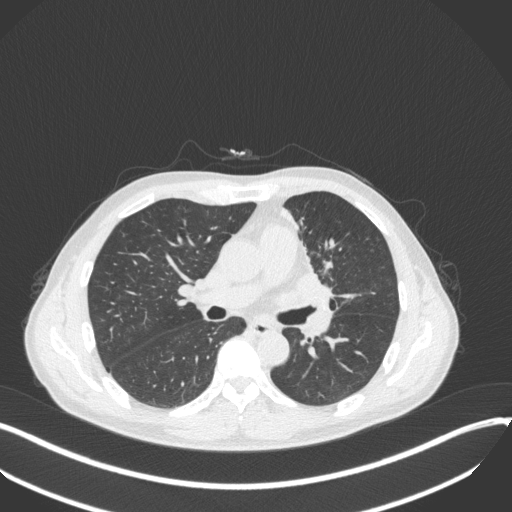
Chest CT, one axial slice; position 188 of 411 along the scan axis; reconstruction kernel B31f; 120 kVp; lung window (W 1500 / L -600 HU); 1 mm slice thickness; 512 × 512 image matrix. Male patient, age 56 years. From the clinical record (not read from this slice): clinical TNM (as recorded): T2a N0 M0.
Annotated regions visible in this slice (bounding box drawn by a radiologist):
- lung tumour (recorded histology: squamous cell carcinoma): box from (x=273, y=265) to (x=339, y=307) px